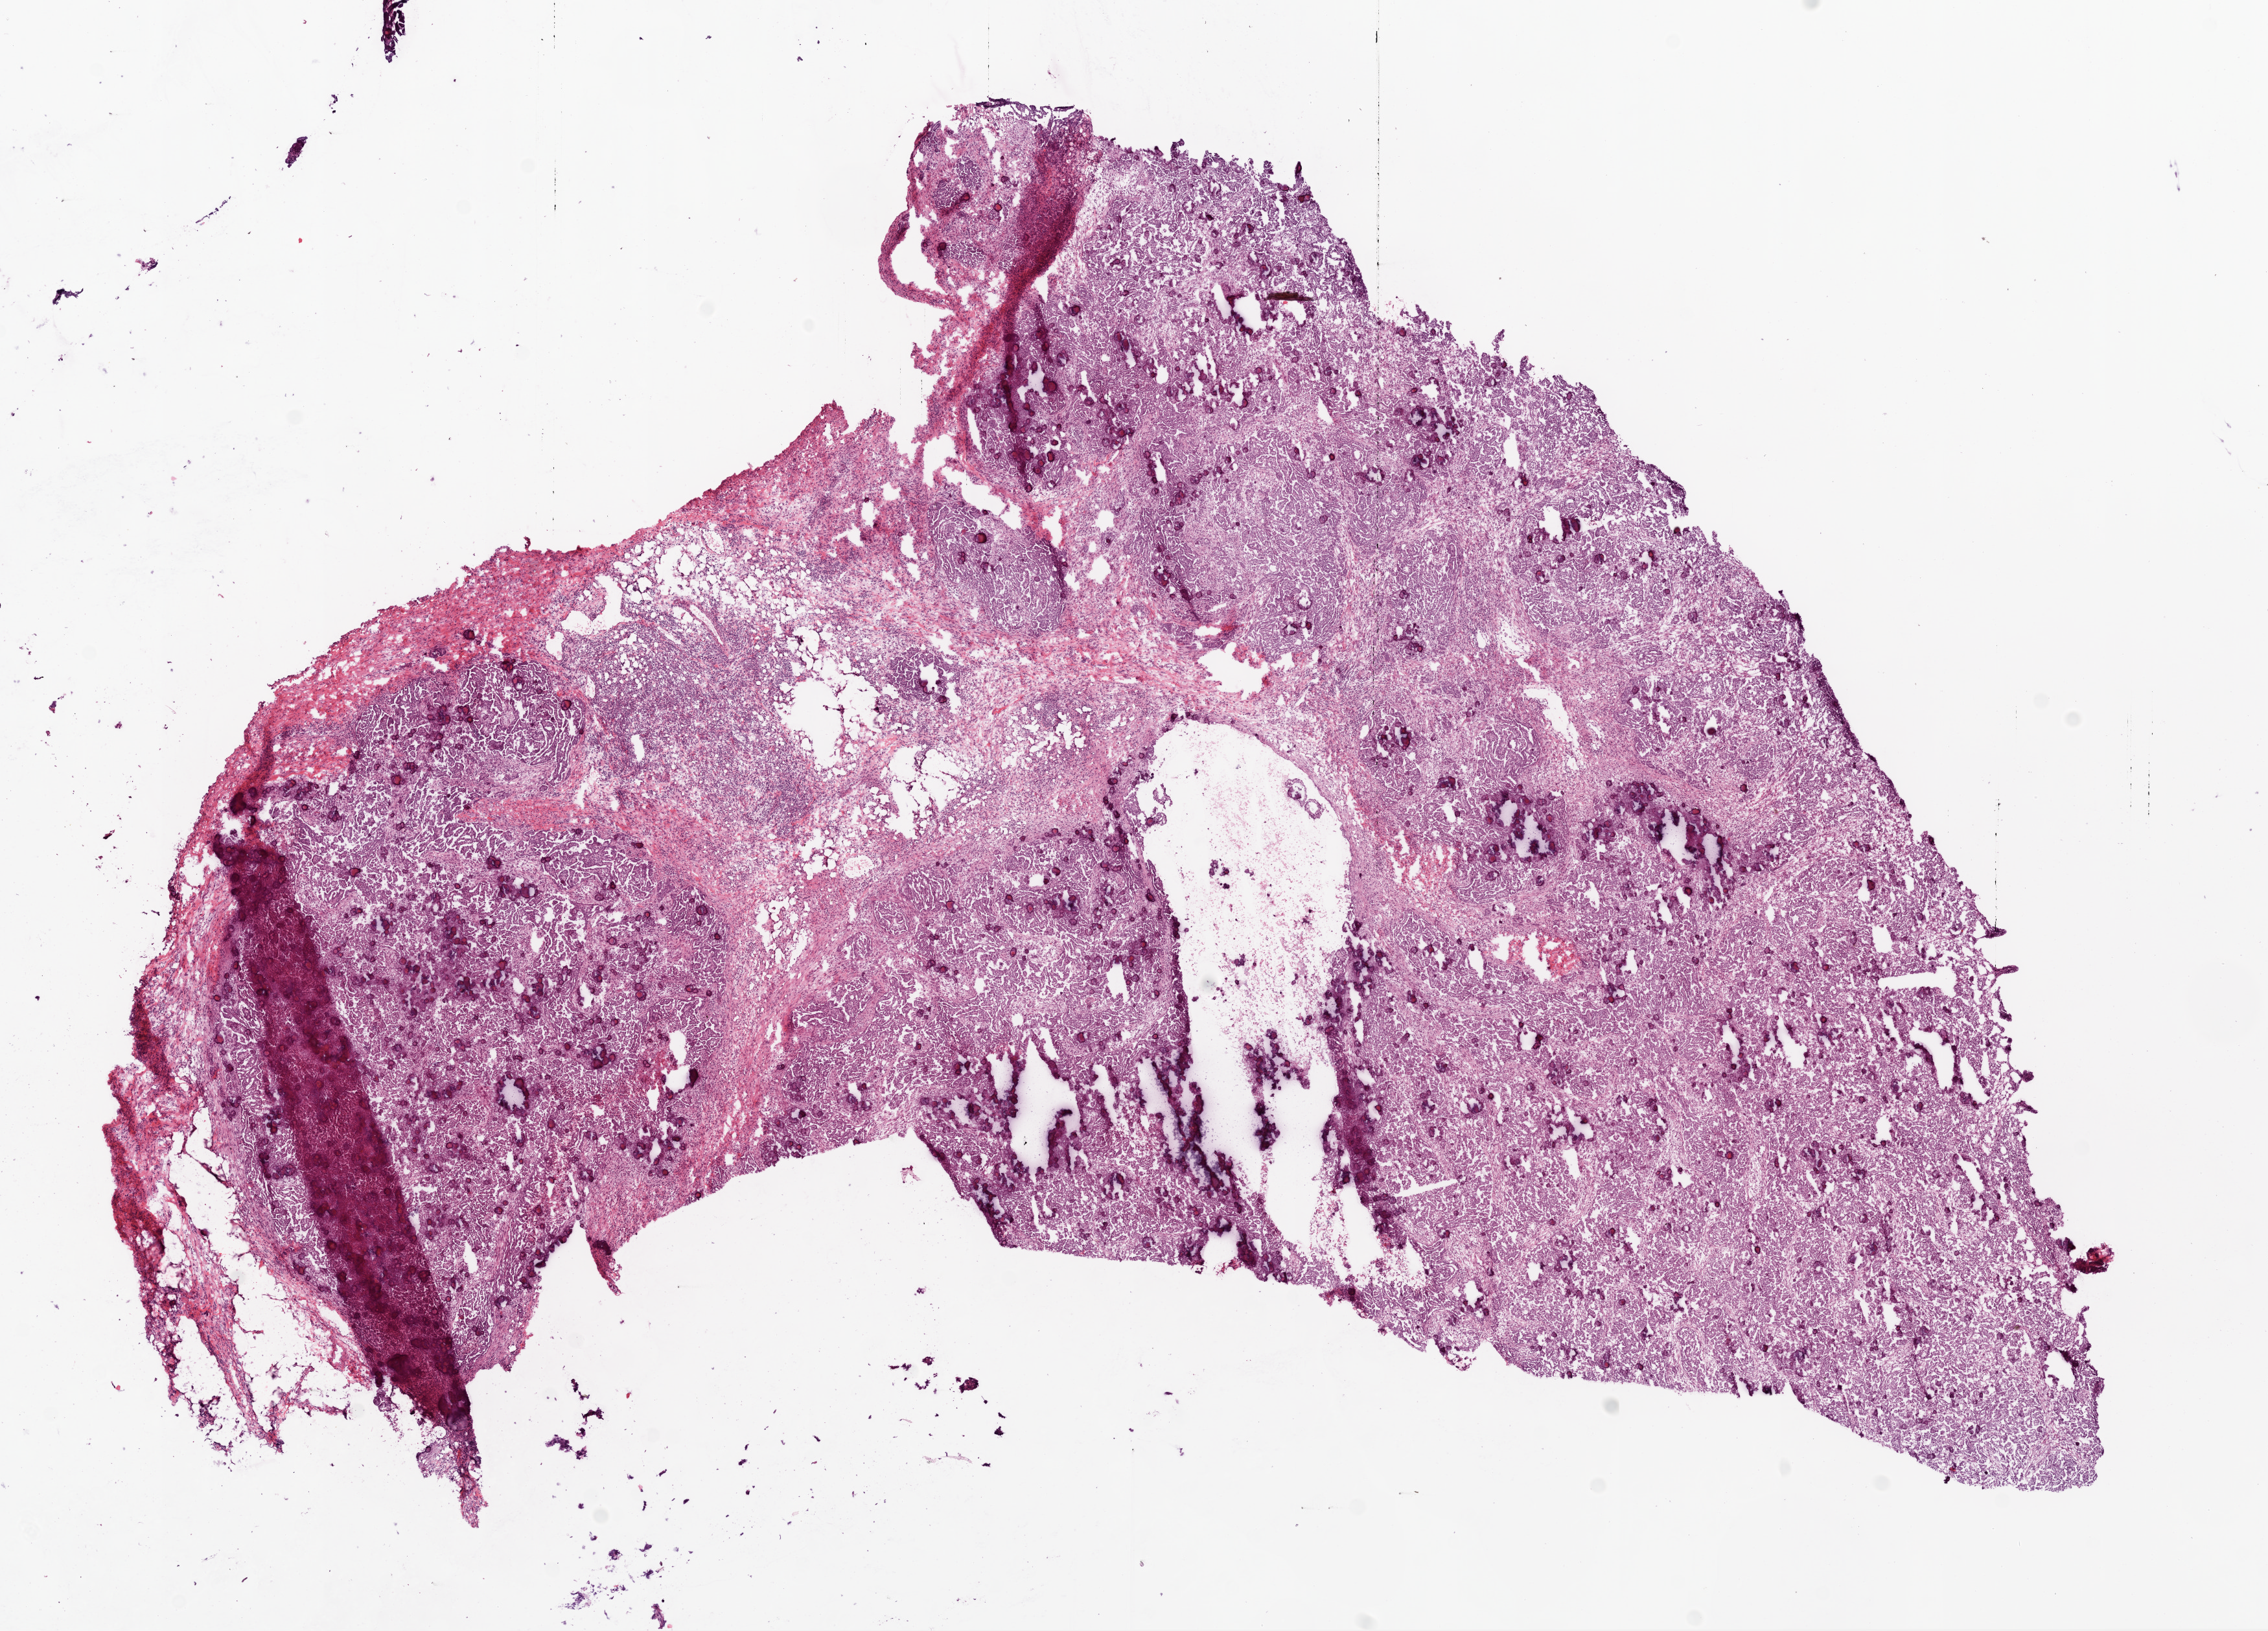
Digitized H&E tissue section (whole slide) — shown as a low-resolution overview of the whole scanned area (about 14.0 x 10.1 mm, from a 20x scan). Frozen section. Primary tumour sample from the ovary. Patient: female, age at initial diagnosis 37 years. Slide review estimates, as recorded: tumour cells 90%, tumour nuclei 90%.
Pathologic diagnosis: Serous cystadenocarcinoma, NOS.